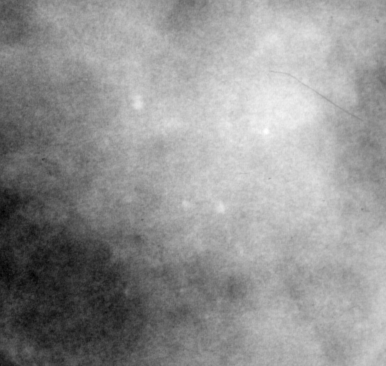
Cropped region of a digitized screen-film mammogram centred on a radiologist-marked abnormality, left breast, CC view.
Calcifications, morphology pleomorphic, distribution clustered; BI-RADS assessment category 4; subtlety rating 2 on a 1 (subtle) to 5 (obvious) scale; pathology result (as recorded, not read from the image): malignant.